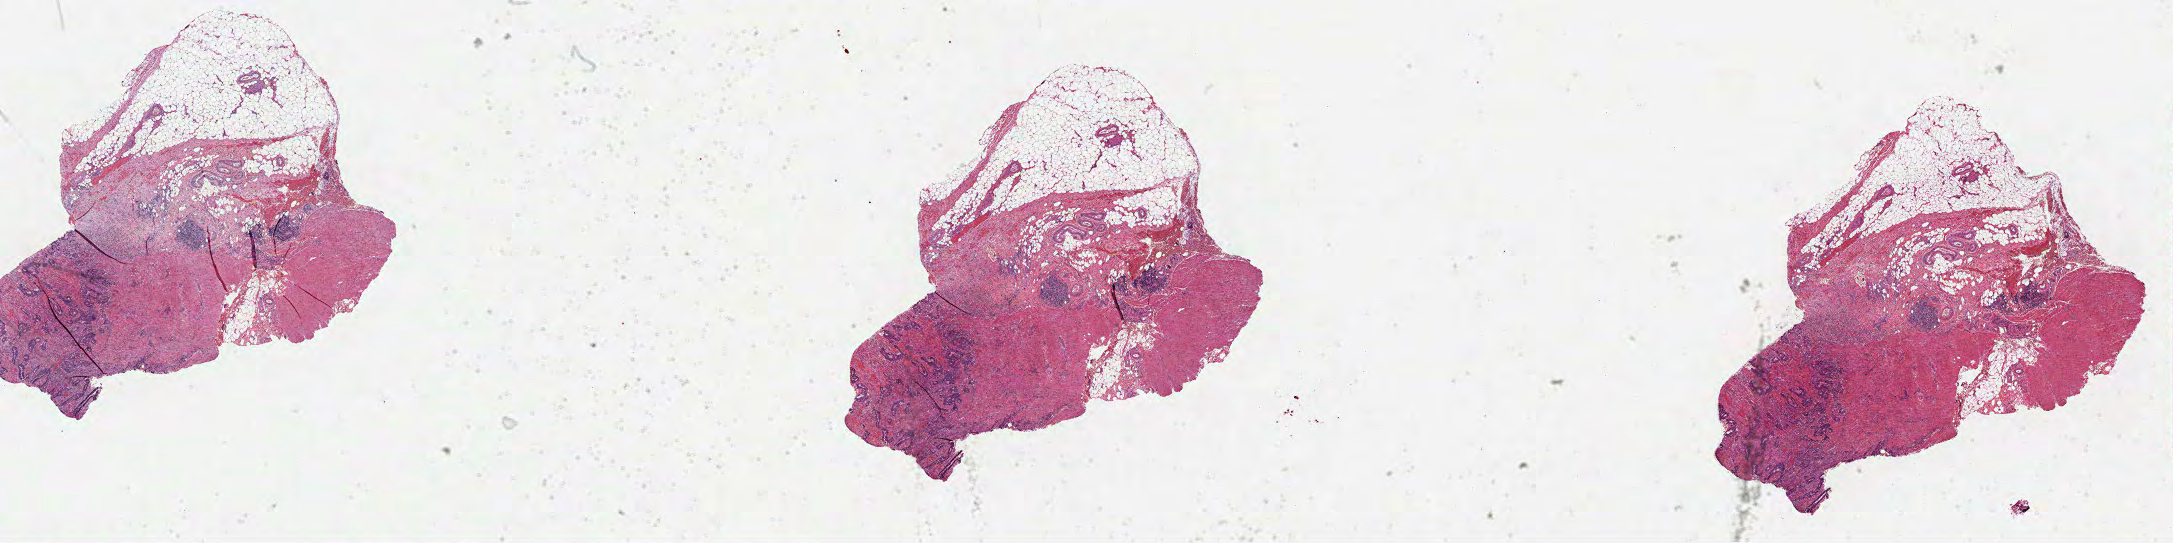
Digitized Hematoxylin and eosin (H&E) stained tissue section (whole slide) — low-resolution overview of the scanned area, about 35.1 x 8.8 mm (acquisition: 40x scan); formalin-fixed paraffin-embedded (FFPE) diagnostic section; rectum, primary tumour sample. Patient: male, age at initial diagnosis 48 years.
• histologic diagnosis: Adenocarcinoma, NOS
• AJCC pathologic stage: IIIC (6th edition)
• lymph nodes positive (case pathology): 9 of 18 examined